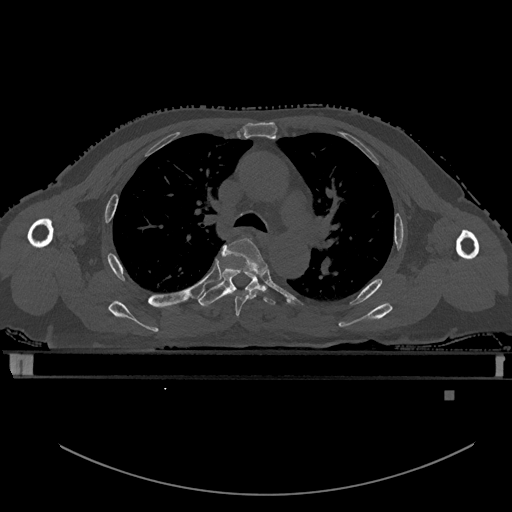
CT including the spine, one axial slice; bone window (W 1800 / L 400 HU); 512 × 512 image matrix, field of view 456 × 456 mm. Patient: male, 82 years. From the clinical record (not read from this slice): primary cancer: prostate; vertebrae with lytic lesions (as recorded): T11, T9, T8, T2.
Annotated regions visible in this slice (semi-automatically segmented with operator editing):
- T4 vertebra: bounding box [x1, y1, x2, y2] px = [222, 238, 268, 318]
- T5 vertebra: [198, 255, 276, 307]